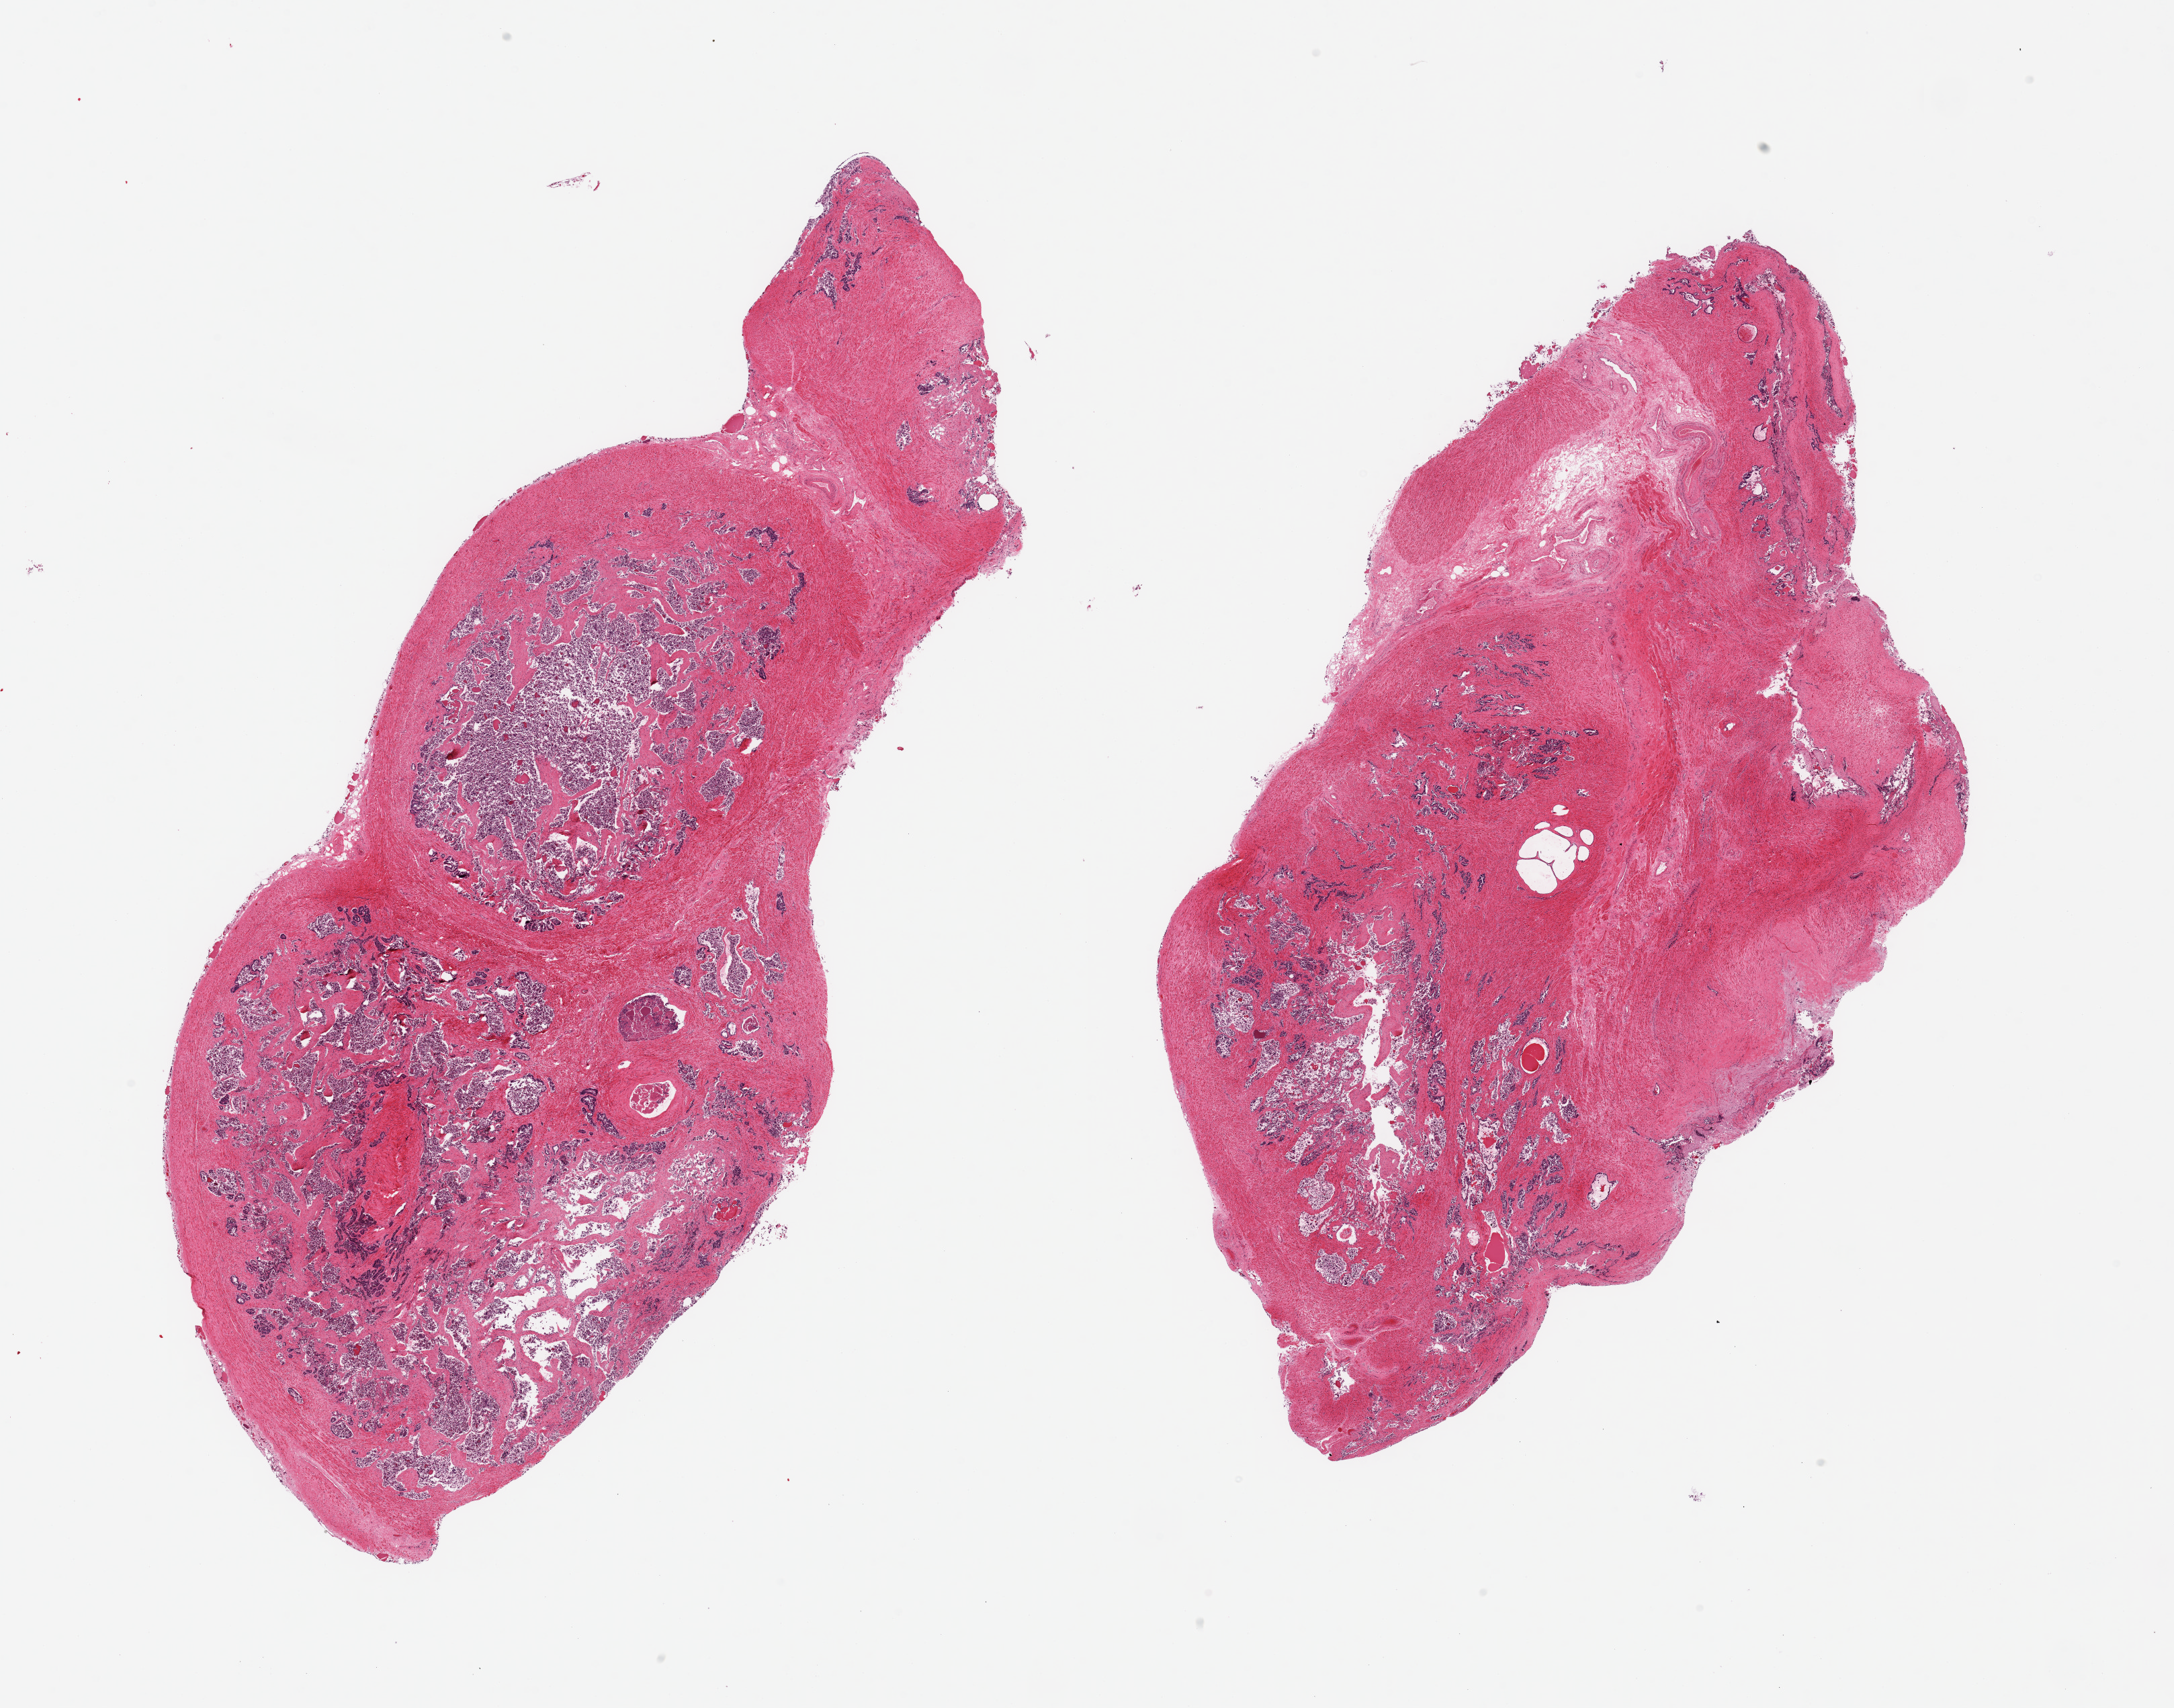
Whole-slide image, haematoxylin and eosin stain, a low-resolution overview of the entire scanned area, about 25.6 x 20.1 mm, PAXgene-fixed, paraffin-embedded tissue, section of prostate (target tissue), tissue donor sample. Donor sex: male.
* reviewer comment on this tissue sample: 2 pieces, advanced glandular autolysis; by pattern and yellow pigment in autolyzed mucosa (rep) this is seminal vesicle, not prostate